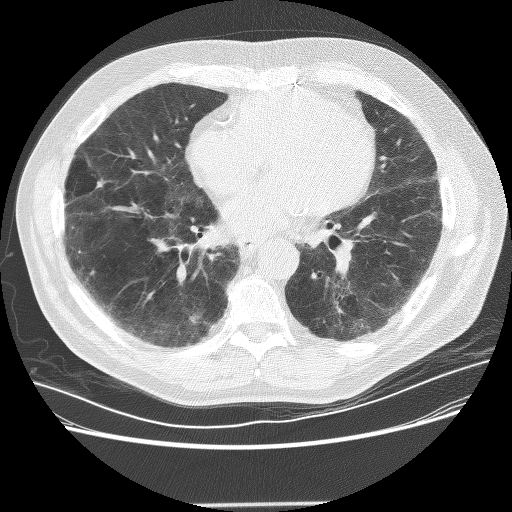
Axial slice from a low-dose chest CT screening exam, first (baseline) screen, lung window (W 1500 / L -600 HU), 512 × 512 image matrix, field of view 370 × 370 mm. Male participant, aged 72 years at enrolment. Former smoker at enrolment.
Expert reader's lesion annotation, bounding box <169,306,210,344> (left, top, right, bottom; pixels). The screening reader recorded 2 non-calcified nodules or masses ≥4 mm on this exam (right lower lobe, left lower lobe); which of them this box marks is not recorded. Official screen result: positive, change unspecified: nodule(s) >= 4 mm or enlarging nodule(s), mass(es), or other non-specific abnormalities suspicious for lung cancer. Later outcome: lung cancer diagnosed 436 days after this screen — squamous cell carcinoma, NOS, right lower lobe, poorly differentiated (G3), stage IB (AJCC 6th edition), 42 mm at pathology.